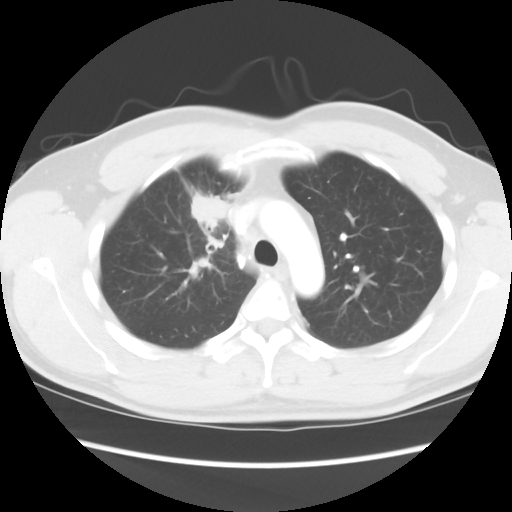
Chest CT, one axial slice; slice 65 of 80 in the series (ordered by position); lung window (W 1500 / L -600 HU); 5 mm slice thickness; 512 × 512 image matrix, field of view 360 × 360 mm. Patient: male, 35 years. From the clinical record (not read from this slice): clinical TNM (as recorded): T1c N1 M1b.
Outlined on this slice (bounding box drawn by a radiologist):
- lung tumour (recorded histology: adenocarcinoma): bounding box (x1, y1, x2, y2) in pixels: (189, 190, 230, 233)